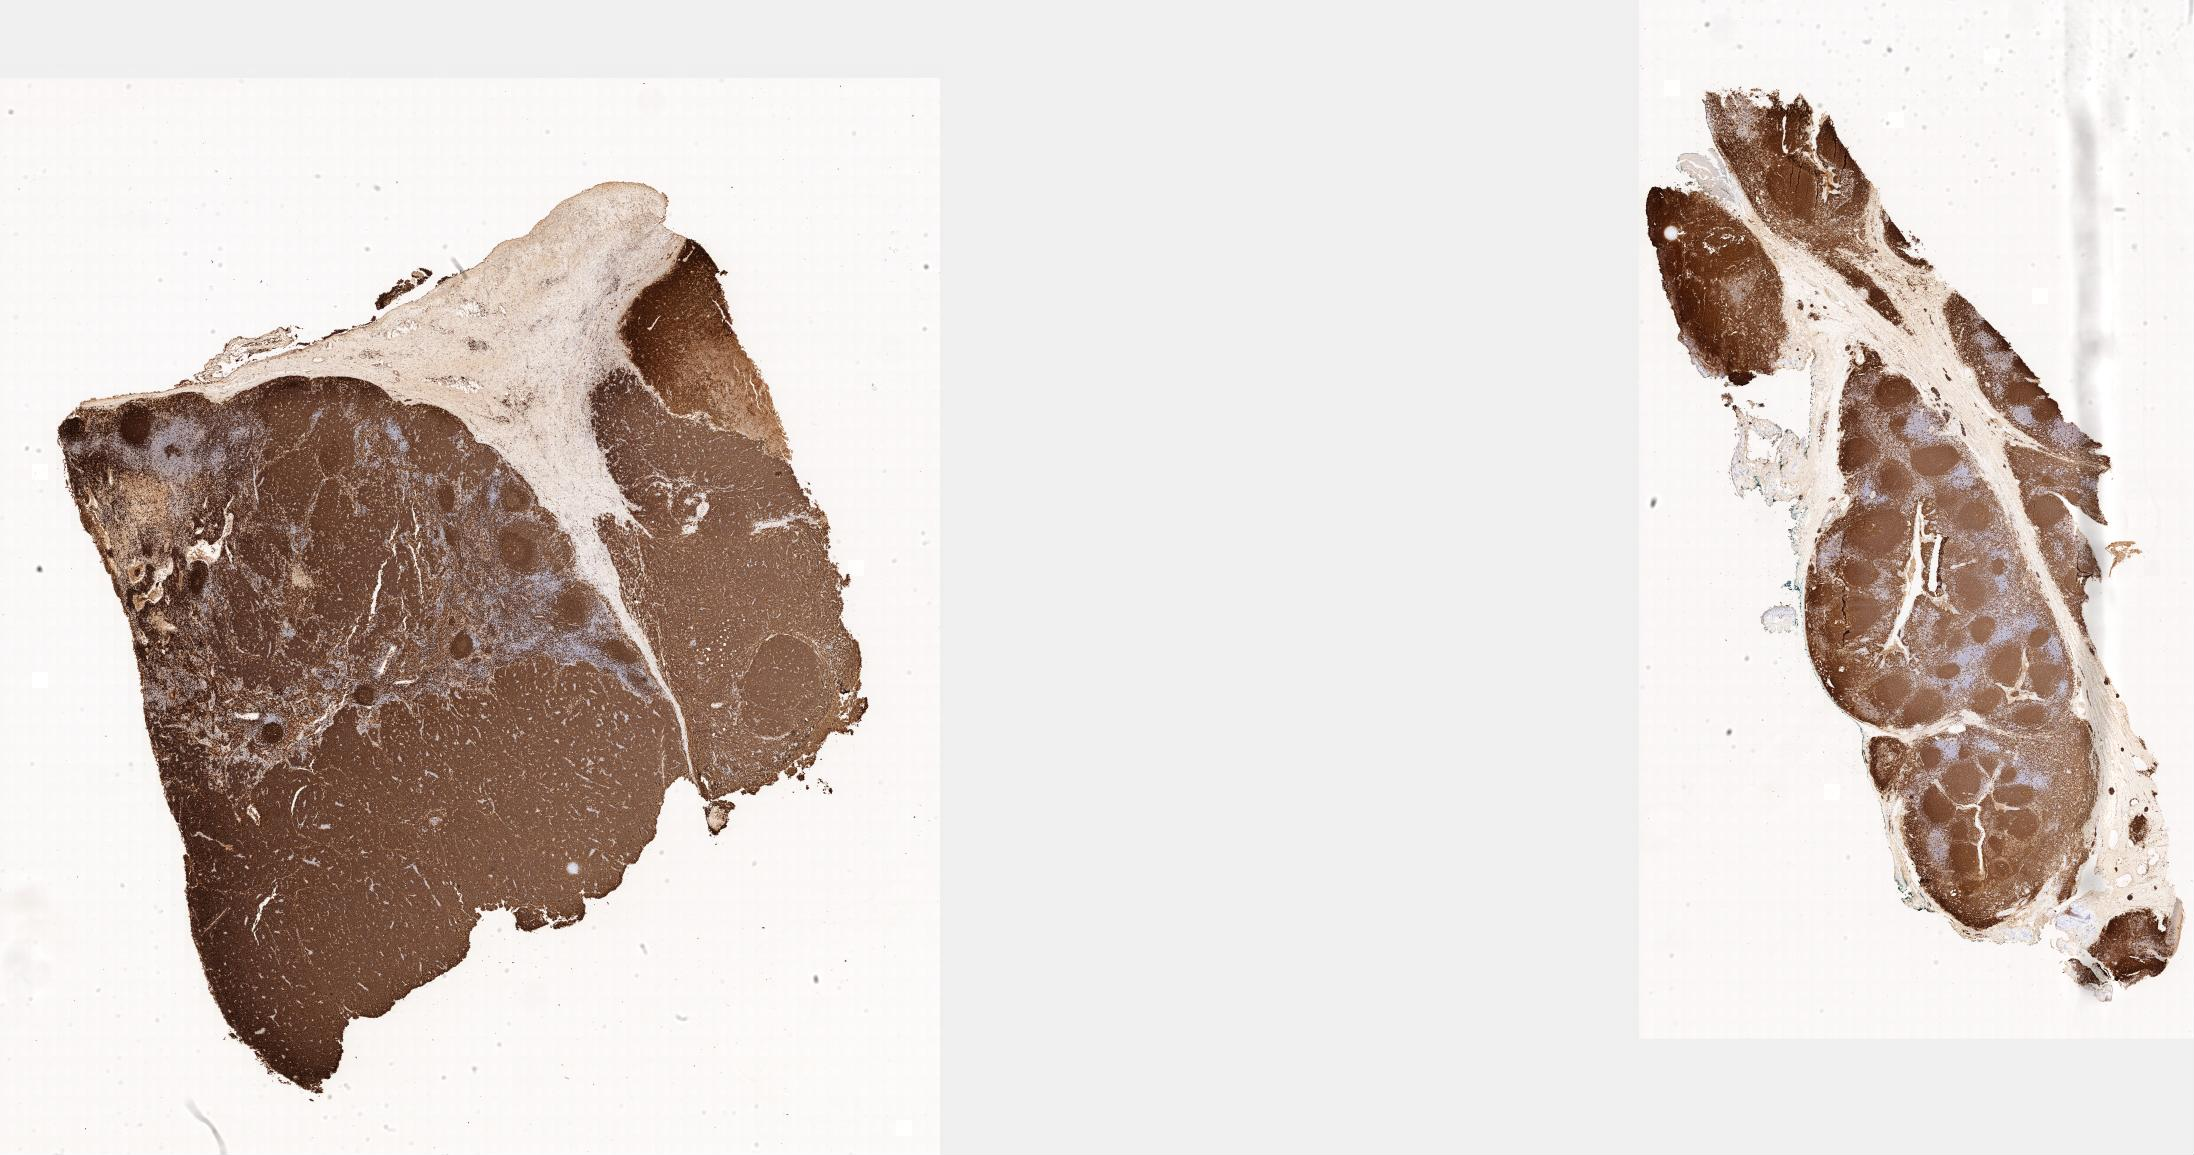
Immunohistochemistry (IHC) whole-slide image stained for CD20 — whole scanned area shown as a low-resolution overview, specimen: tumor tissue, site: abdominal lymph node. Female patient, aged 14.
Histologic diagnosis: Burkitt lymphoma, NOS.